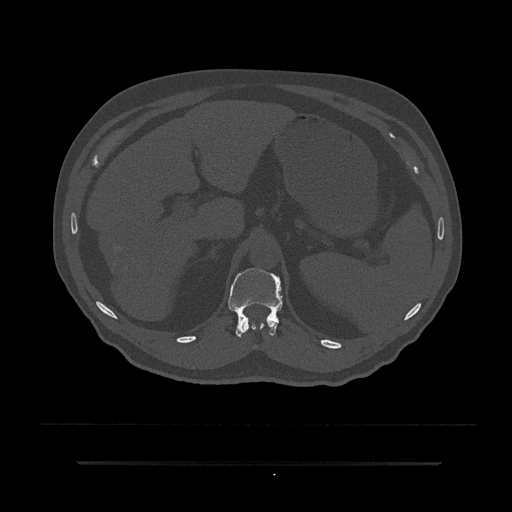
CT including the spine, one axial slice. Slice 234 of 797 in the series (ordered by position). Bone window (W 1800 / L 400 HU). 0.5 mm slice thickness. 512 × 512 image matrix. Patient: male, 59 years. Case-level facts recorded for this patient, not image findings: primary cancer: bile ducts.
Outlined on this slice (semi-automatic segmentation, software-assisted and operator-edited):
- T11 vertebra: bounding box <244,318,278,331> (left, top, right, bottom; pixels)
- T12 vertebra: <228,268,282,337>